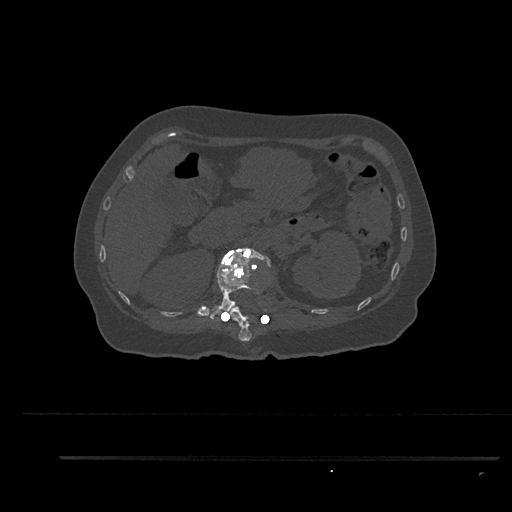
CT including the spine, one axial slice; position 233 of 797 along the scan axis; reconstruction kernel Br40s/3; 120 kVp; bone window (W 1800 / L 400 HU); 0.5 mm slice thickness; 512 × 512 image matrix, field of view 408 × 408 mm. Female patient, age 44 years. From the clinical record (not read from this slice): primary cancer: renal.
Structures marked on this image (semi-automatic segmentation, software-assisted and operator-edited):
- L1 vertebra: box from (x=209, y=247) to (x=271, y=322) px
- T12 vertebra: (x=219, y=307)–(x=253, y=341)